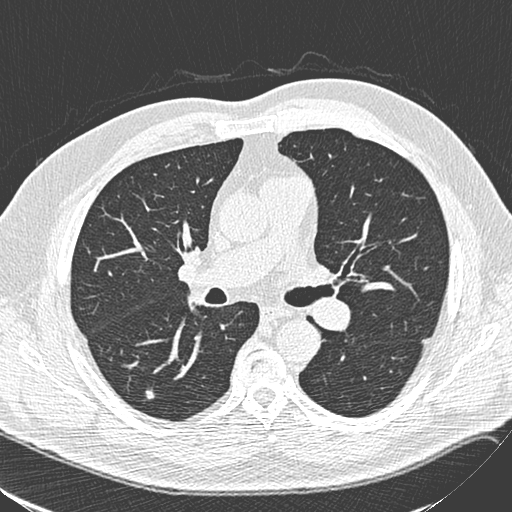
Low-dose screening chest CT, one axial slice. Slice 151 of 248 in the series (ordered by position). 120 kVp. Lung window (W 1500 / L -600 HU). 1.3 mm slice thickness. 512 × 512 image matrix, field of view 357 × 357 mm.
Structures marked on this image (expert manual segmentation):
- lesion 1 (tumor, lower lobe of right lung): bounding box (x1, y1, x2, y2) in pixels: (146, 390, 155, 399)